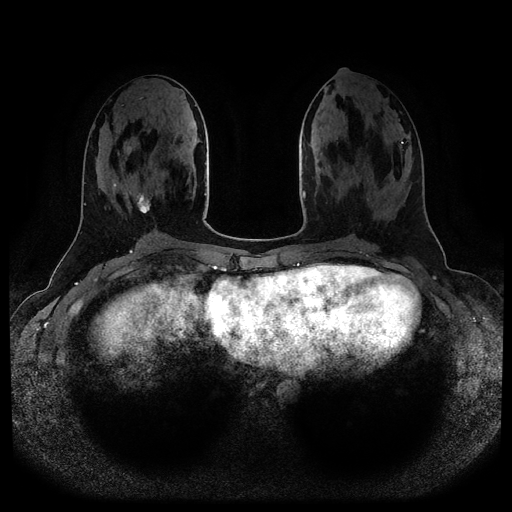
Breast MRI (dynamic contrast-enhanced, multi-phase), one axial slice. Slice 42 of 116 in the series (ordered by position). Dynamic contrast-enhanced series, time point 2 of 5 at this slice position (early post-contrast). 1.5 T. TE 2.6 ms, TR 5.2 ms. 2 mm slice thickness. 512 × 512 image matrix, field of view 380 × 380 mm. Patient: female, 25 years.
Outlined on this slice (semi-automatically segmented with operator editing):
- breast lesion (labelled benign in the annotation): box from (x=136, y=193) to (x=151, y=214) px